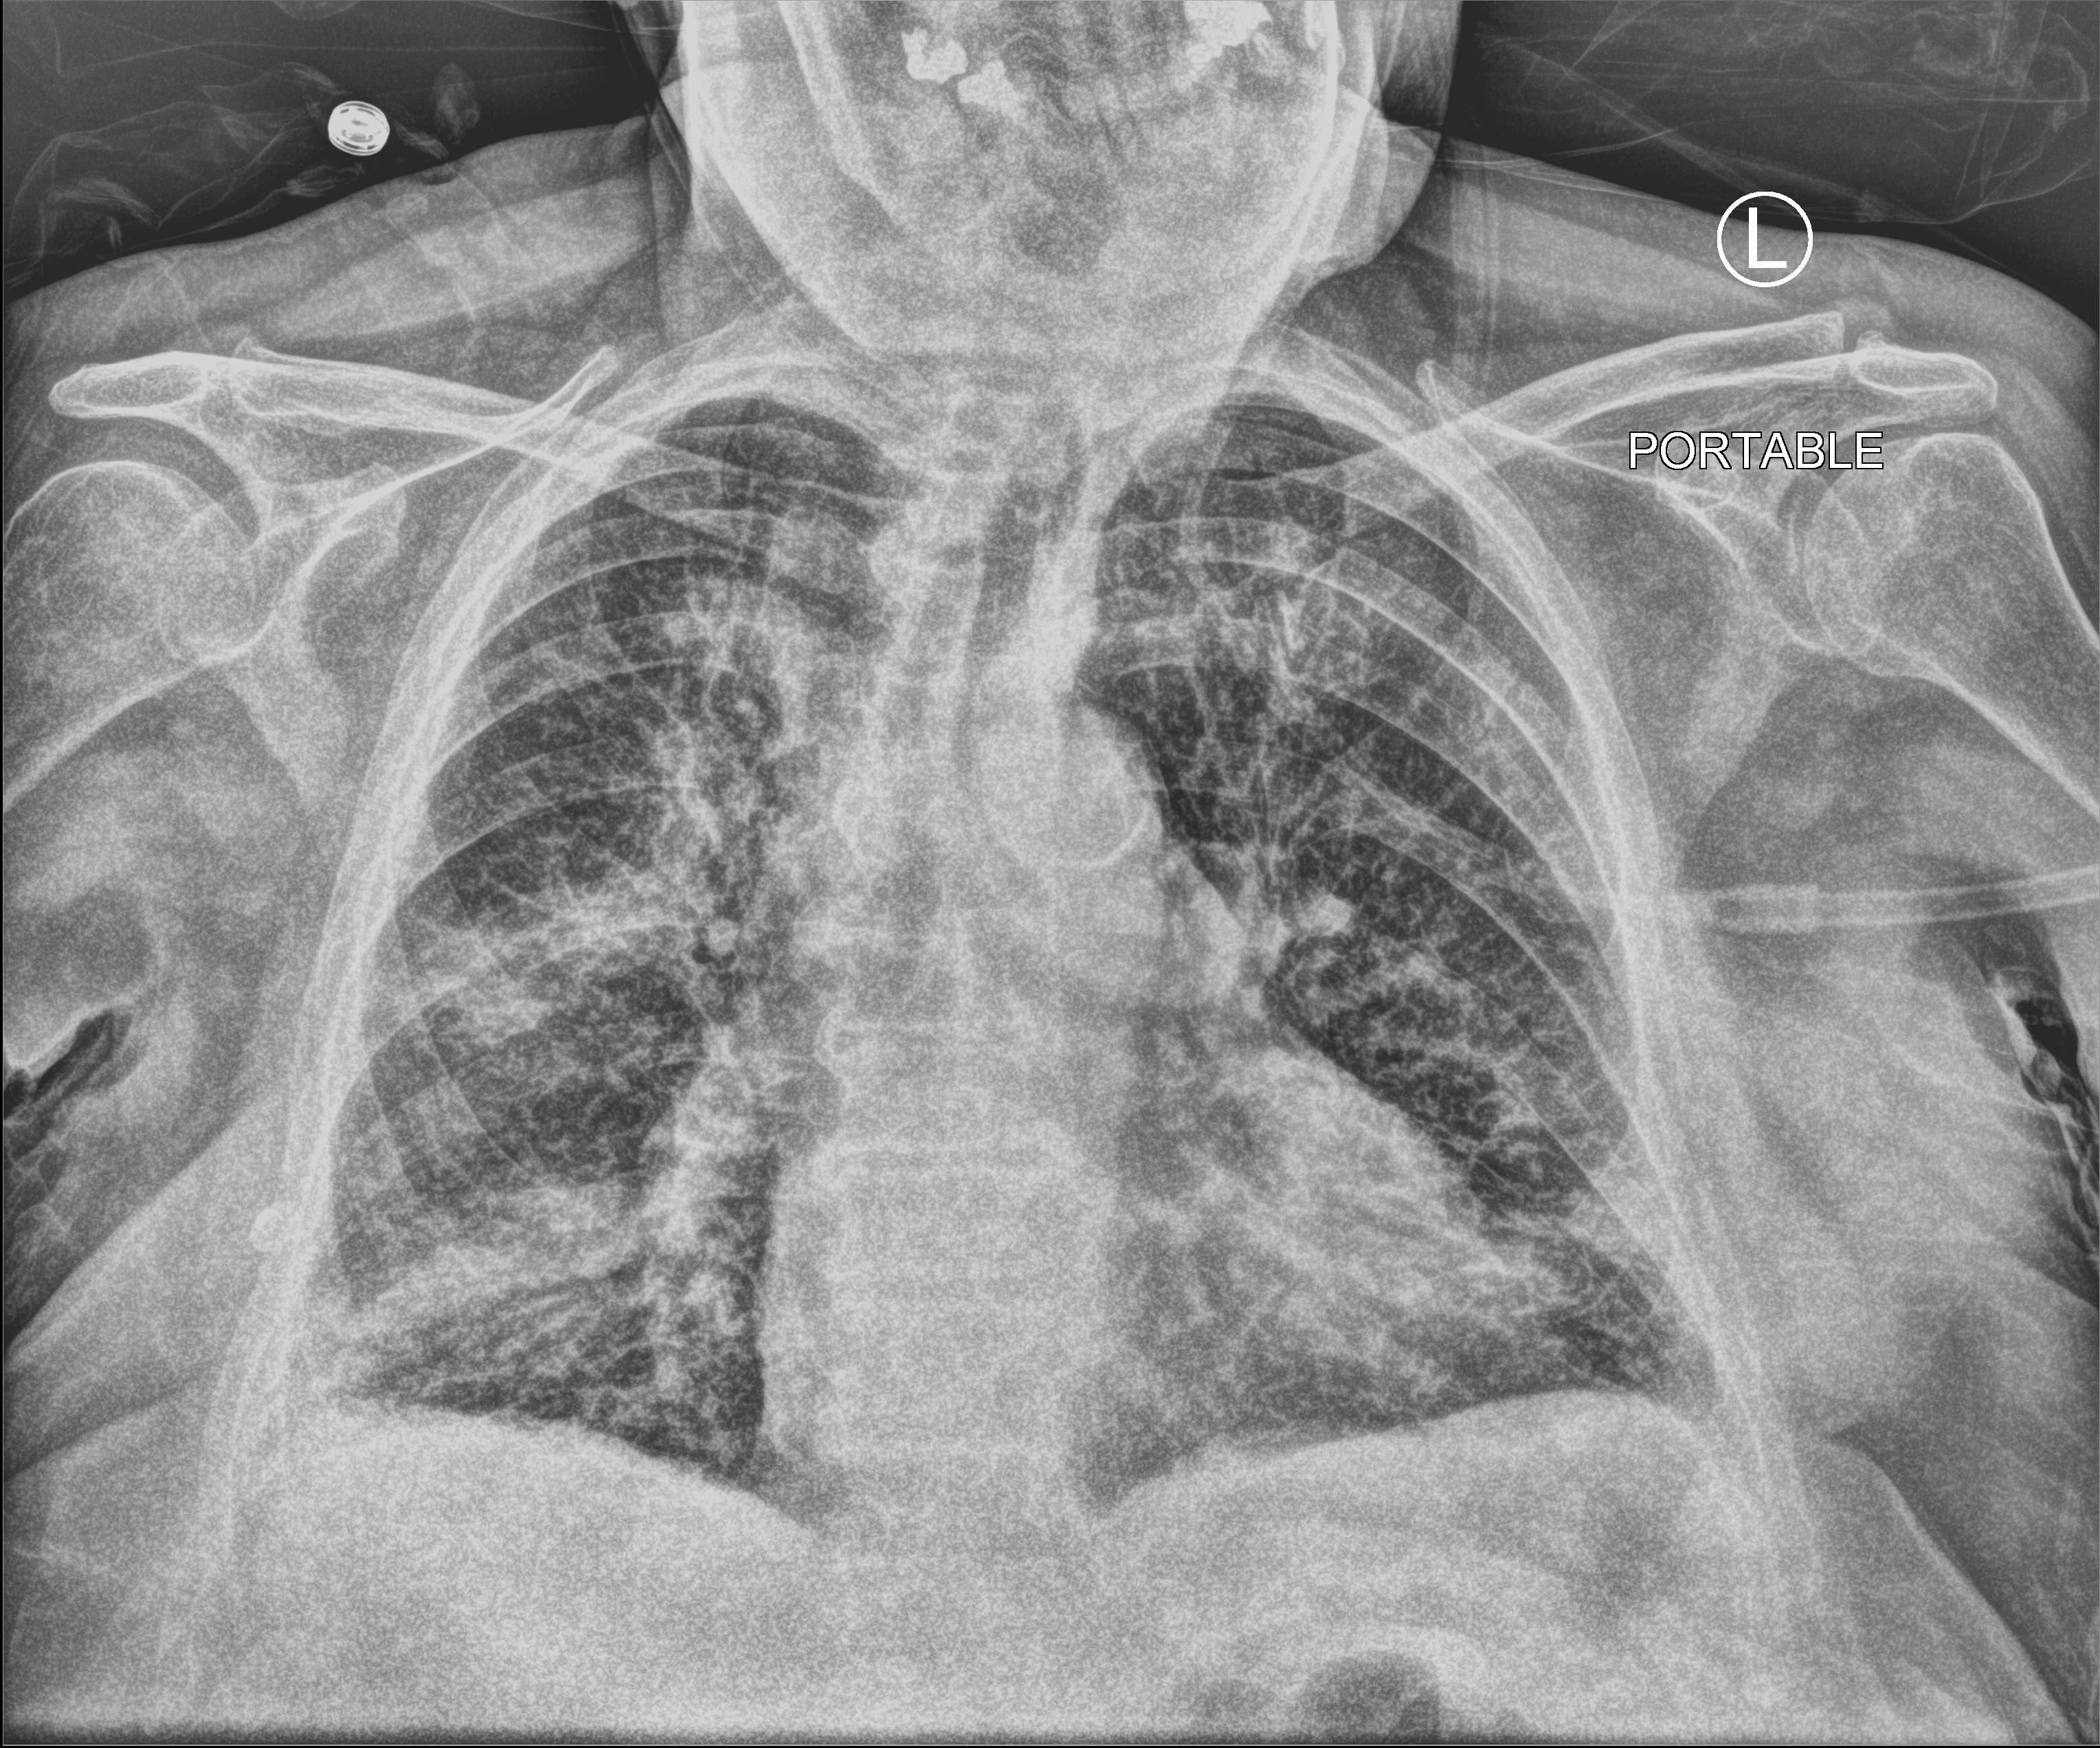
Chest X-ray (portable); anteroposterior (AP) projection. Female patient hospitalised with COVID-19, age 75–90 years.
Hospital-stay facts (about this admission, not read from this image; timing relative to this image not recorded): admitted to intensive care during this hospital stay: no; mechanically ventilated during this hospital stay: no.